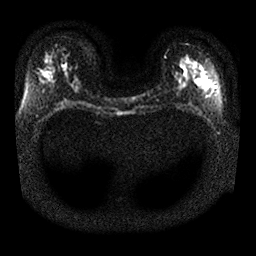
Breast MRI, one axial slice. Position 15 of 25 along the scan axis. Diffusion-weighted series; image 2 of 4 stored at this slice position (different b-values; order by instance number). 1.5 T. 4 mm slice thickness. 256 × 256 image matrix, field of view 340 × 340 mm. Female patient.
Annotated regions visible in this slice (manually delineated by an expert):
- tumour on diffusion-weighted imaging: box from (x=44, y=72) to (x=51, y=78) px